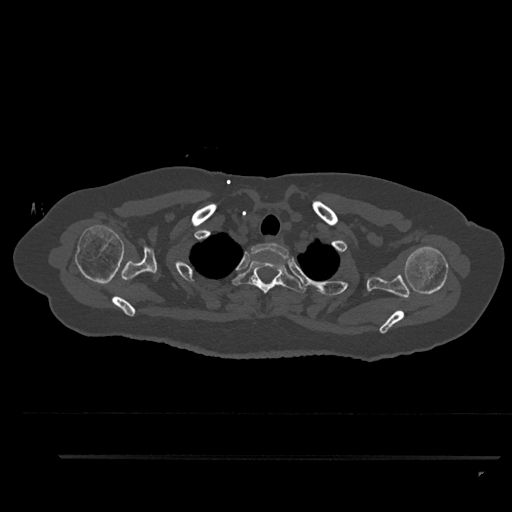
CT including the spine, one axial slice; position 733 of 797 along the scan axis; 120 kVp; bone window (W 1800 / L 400 HU); 0.5 mm slice thickness; 512 × 512 image matrix, field of view 408 × 408 mm. Female patient, age 44 years. From the clinical record (not read from this slice): primary cancer: renal; vertebrae with lytic lesions (as recorded): L1.
Structures marked on this image (semi-automatic segmentation, software-assisted and operator-edited):
- T1 vertebra: bounding box <249,243,289,262> (left, top, right, bottom; pixels)
- T2 vertebra: <232,260,306,294>